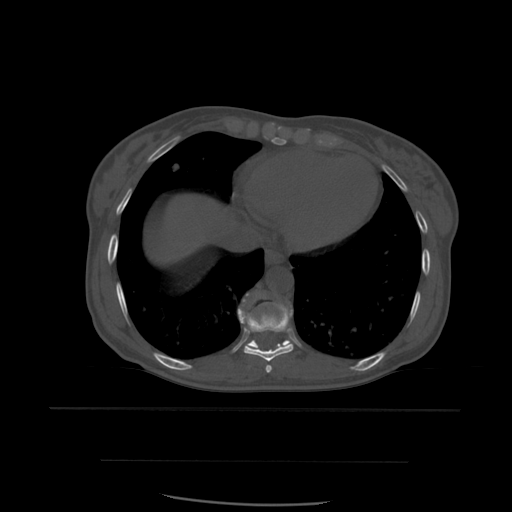
CT including the spine, one axial slice; position 331 of 574 along the scan axis; bone window (W 1800 / L 400 HU); 1.25 mm slice thickness; 512 × 512 image matrix, field of view 392 × 392 mm. Patient age 48 years. Case-level facts recorded for this patient, not image findings: primary cancer: lung; vertebrae with lytic lesions (as recorded): T11.
Outlined on this slice (semi-automatic segmentation, software-assisted and operator-edited):
- T10 vertebra: box from (x=238, y=301) to (x=289, y=348) px
- T8 vertebra: (x=266, y=365)–(x=273, y=373)
- T9 vertebra: (x=239, y=294)–(x=294, y=362)